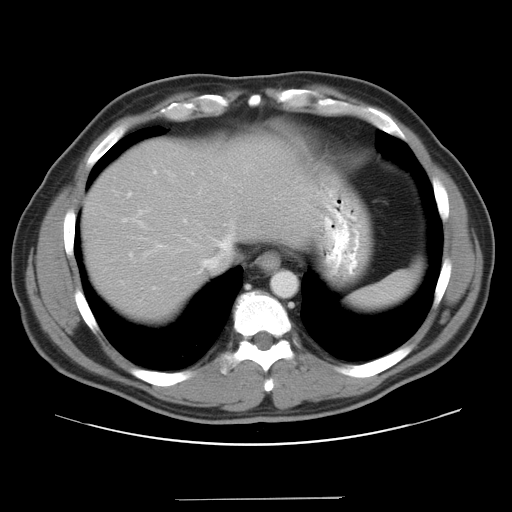
Contrast-enhanced abdominal CT, one axial slice. Slice 33 of 37 in the series (ordered by position). Reconstruction kernel STANDARD. 120 kVp. Soft-tissue window (W 400 / L 40 HU). 7.5 mm slice thickness. 512 × 512 image matrix, field of view 400 × 400 mm. Male patient, age 46 years. Case-level facts recorded for this patient, not image findings: diagnosis: colorectal cancer liver metastases, imaged before liver resection; multiple liver metastases: yes; largest metastasis: 1 cm; chemotherapy before resection: yes.
Annotated regions visible in this slice (manually delineated by an expert):
- hepatic veins: box from (x=160, y=164) to (x=251, y=273) px
- liver: (x=85, y=137)–(x=294, y=316)
- planned liver remnant (the part of the liver to remain after resection): (x=85, y=138)–(x=296, y=316)
- portal vein (with intrahepatic branches): (x=122, y=170)–(x=157, y=227)
- liver metastasis: (x=250, y=228)–(x=257, y=236)